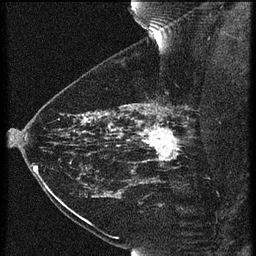
Breast MRI (dynamic contrast-enhanced), one sagittal slice. Slice 45 of 60 in the series (ordered by position). 3 images stored at this slice position (order not interpretable as contrast timing). 1.5 T. TE 4.2 ms, TR 21.3 ms. 1.5 mm slice thickness. 256 × 256 image matrix, field of view 180 × 180 mm. Patient: female, 43 years. Case-level facts recorded for this patient, not image findings: setting: breast cancer imaged before/during neoadjuvant chemotherapy; receptor status: HER2-positive.
Outlined on this slice (semi-automatic segmentation, software-assisted and operator-edited):
- analysis volume of interest (the breast-tissue region the enhancement analysis was run in; not a lesion): bounding box <119,114,189,173> (left, top, right, bottom; pixels)
- tumour enhancement mask (voxels above the 90 % enhancement threshold inside the analysis volume of interest): <119,114,180,173>